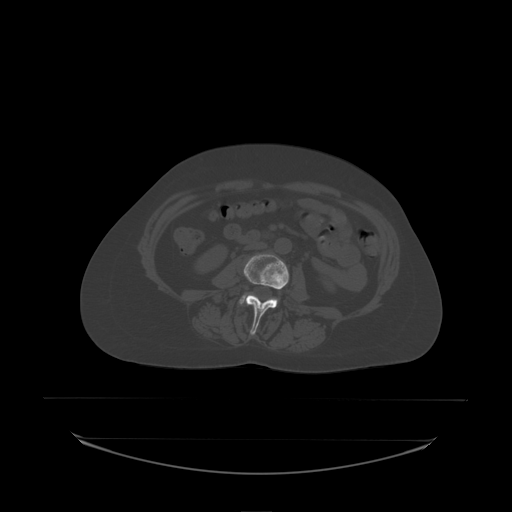
CT including the spine, one axial slice. Slice 59 of 242 in the series (ordered by position). Bone window (W 1800 / L 400 HU). 2.5 mm slice thickness. 512 × 512 image matrix, field of view 500 × 500 mm. Patient: female, 53 years. Case-level facts recorded for this patient, not image findings: primary cancer: lung; vertebrae with lytic lesions (as recorded): T7, L1.
Outlined on this slice (semi-automatic segmentation, software-assisted and operator-edited):
- L3 vertebra: bounding box (x1, y1, x2, y2) in pixels: (244, 254, 290, 336)
- L4 vertebra: (239, 293, 249, 305)